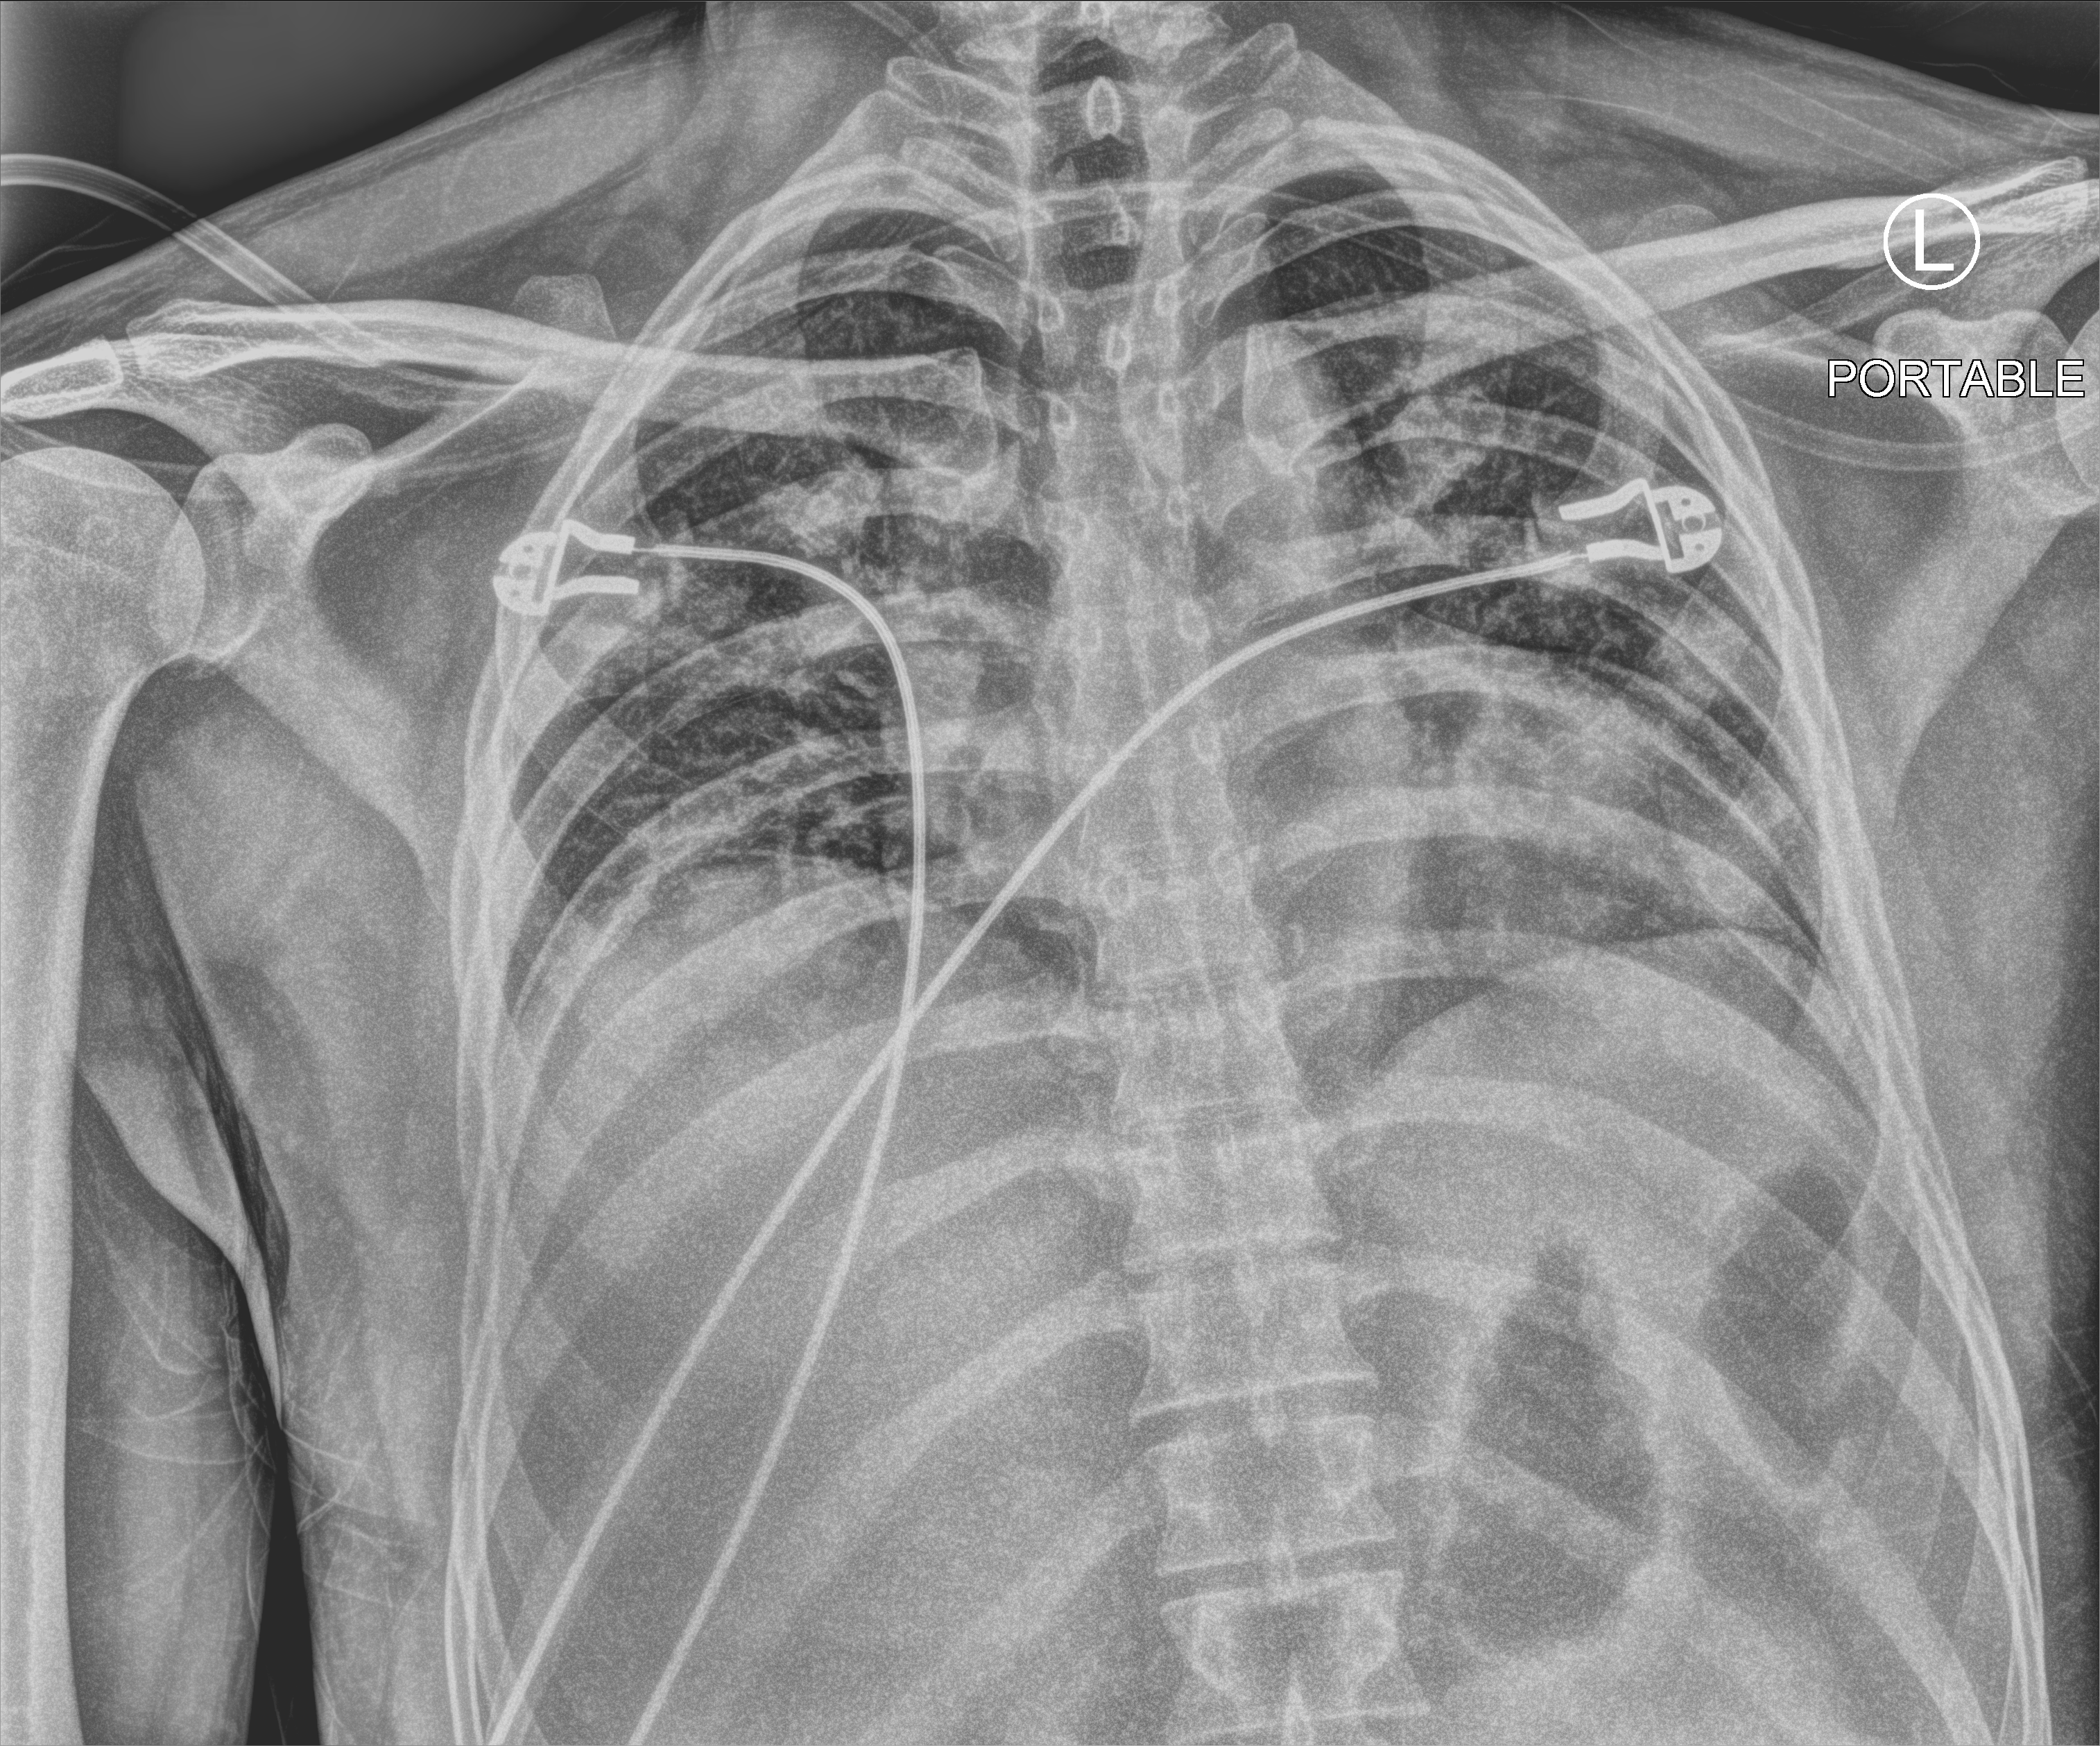
Bedside chest radiograph (computed radiography), anteroposterior (AP) projection. Patient hospitalised with COVID-19; male, aged 18–59 years.
From the hospital-stay record, not from the radiograph (when in the stay this image was taken is not recorded):
- hypertension (admission record): no
- mechanically ventilated during this hospital stay: no
- admitted to intensive care during this hospital stay: no